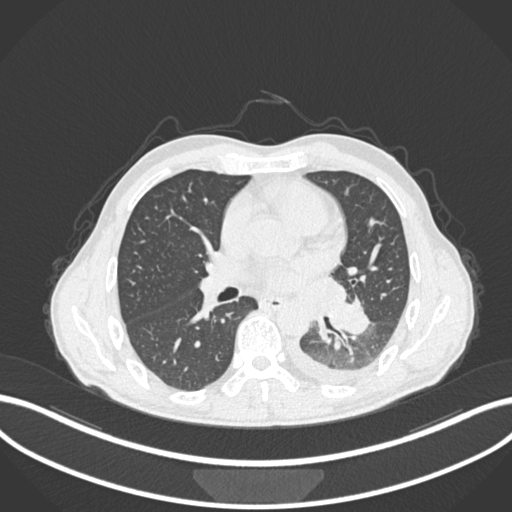
Chest CT, one axial slice; slice 124 of 222 in the series (ordered by position); reconstruction kernel B30f; 120 kVp; lung window (W 1500 / L -600 HU); 1 mm slice thickness; 512 × 512 image matrix, field of view 400 × 400 mm. Patient: male, 47 years. Case-level facts recorded for this patient, not image findings: clinical TNM (as recorded): T3 N1 M1c.
Outlined on this slice (rectangle marked by the reading radiologist):
- lung tumour (recorded histology: small cell carcinoma): bounding box (x1, y1, x2, y2) in pixels: (325, 293, 374, 335)